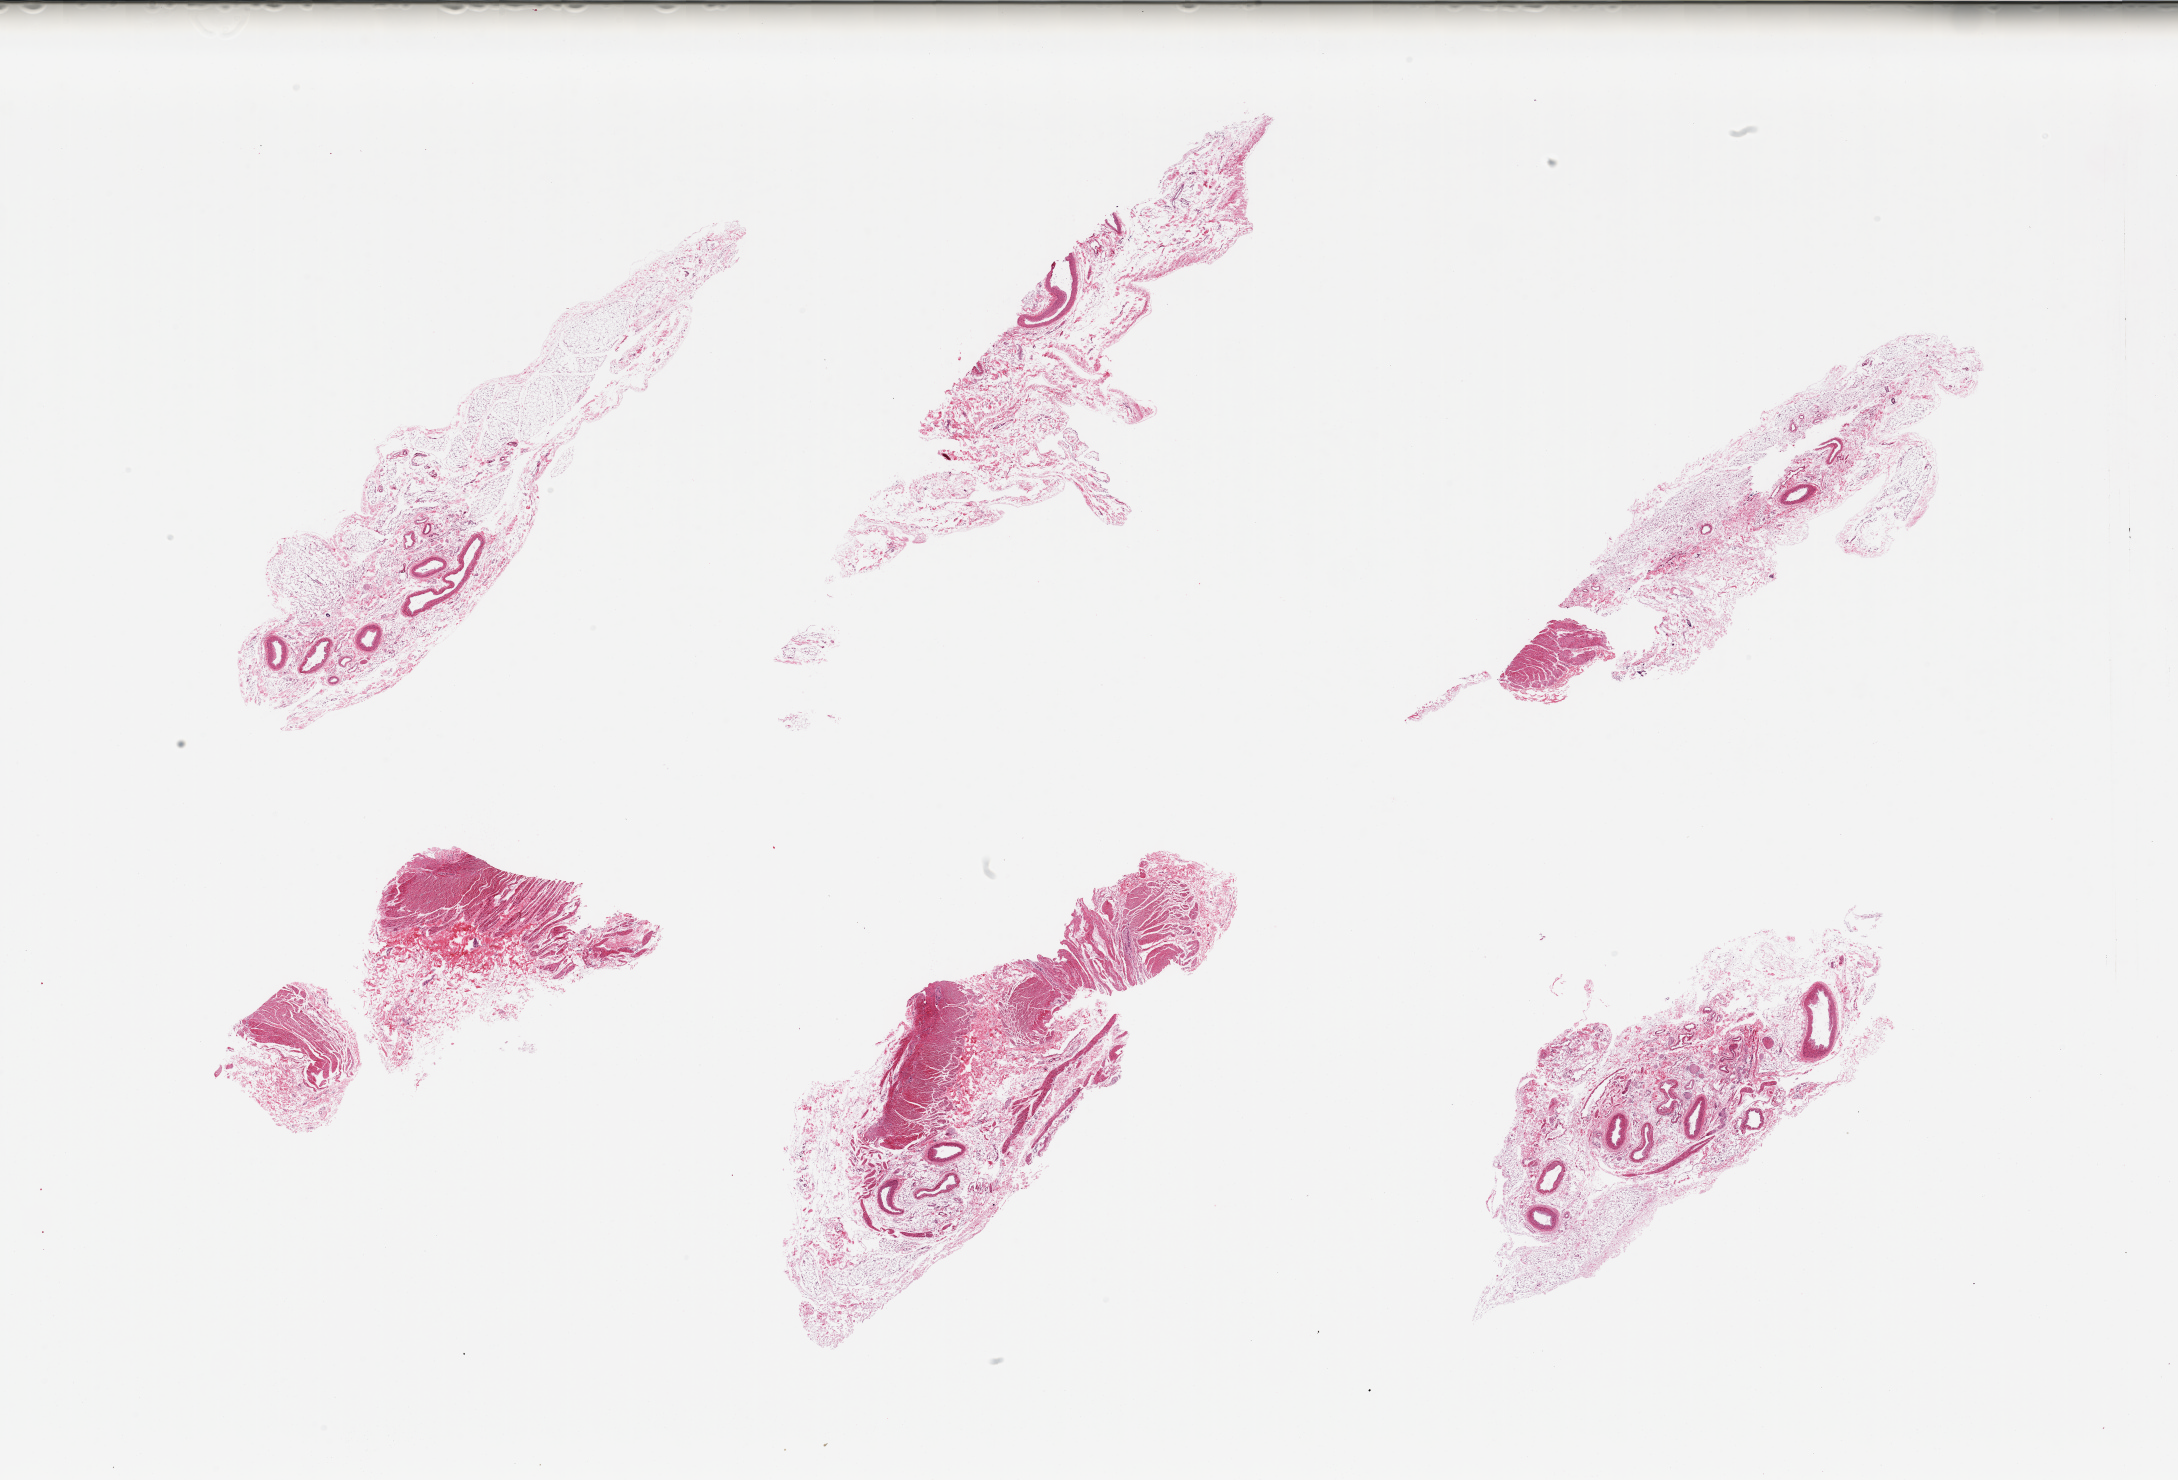
Whole-slide image, hematoxylin and eosin (H&E) stain, whole scanned area (about 34.5 x 23.4 mm) shown as a low-resolution overview. PAXgene-fixed paraffin-embedded (PFPE) section. Sampled site (target tissue): ileum. Tissue donor sample. Donor: male.
Review note (as recorded): 6 pieces; fibrovascular and adipose tissue, muscularis and nerves; target lymphoid aggregates not present.